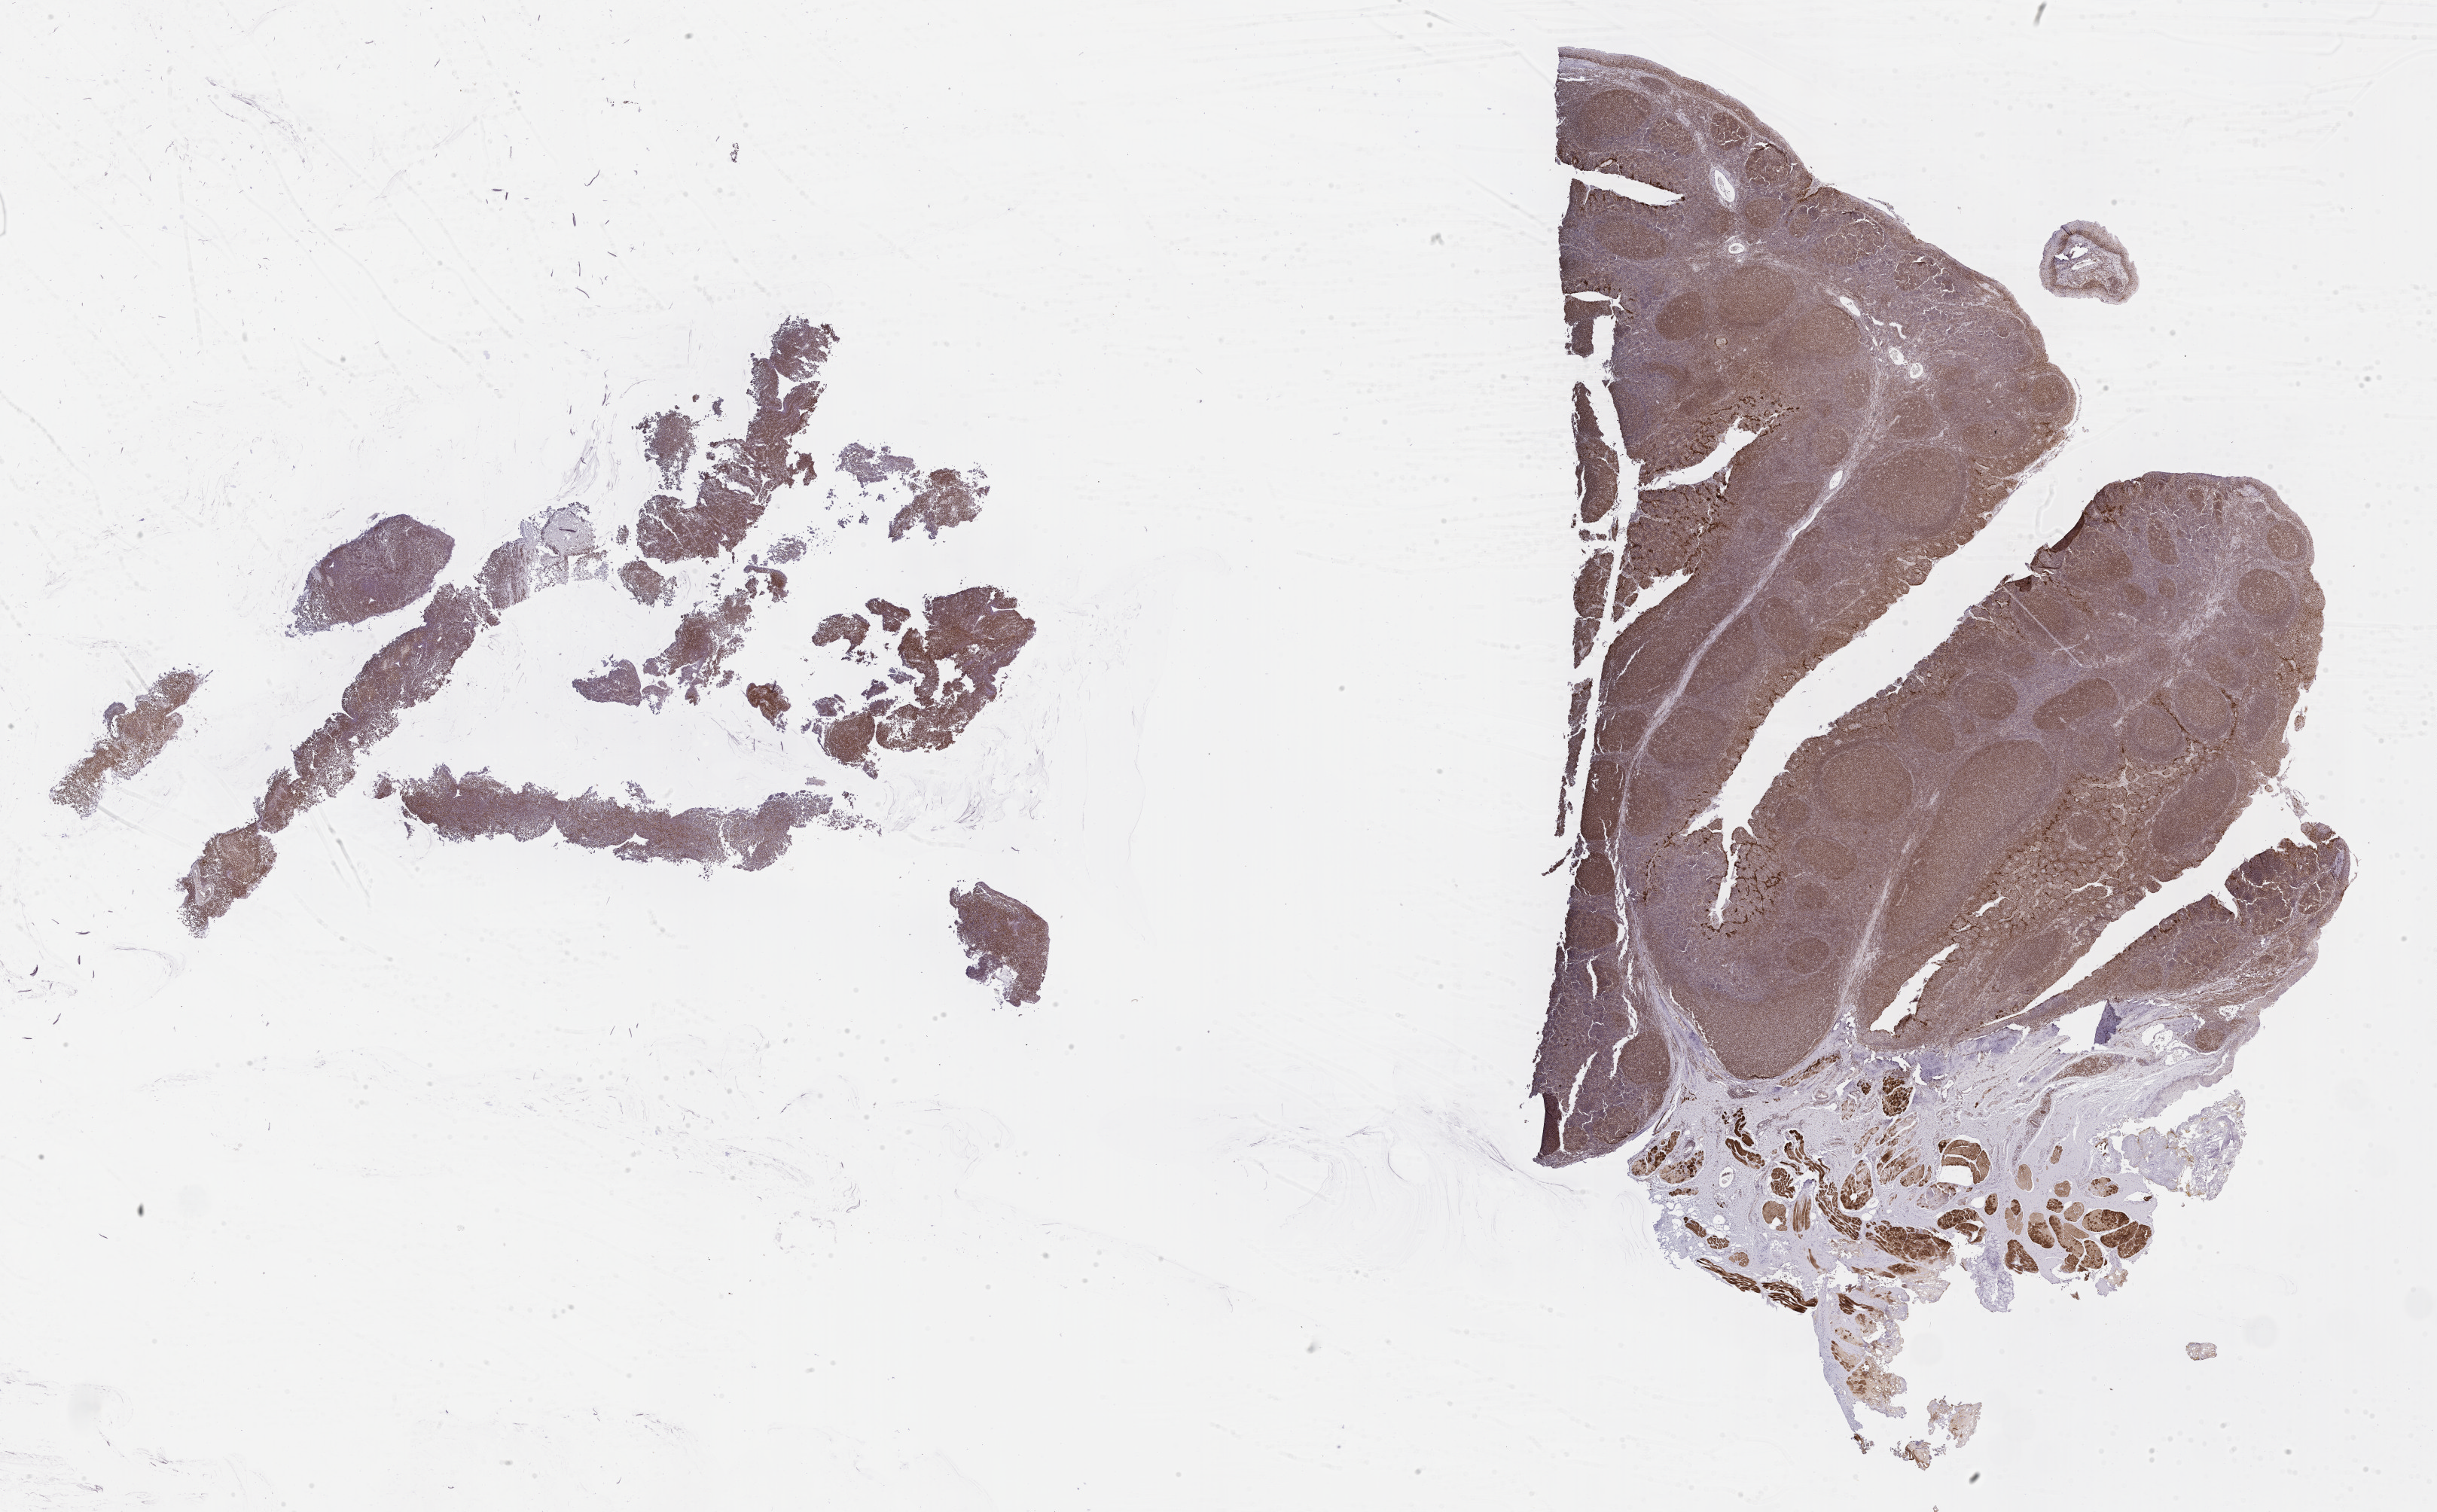
Immunohistochemistry (IHC) whole-slide image stained for BCL6, a low-resolution overview of the entire scanned area, about 26.2 x 16.2 mm. Tumor tissue. Anatomic site: kidney. Patient: male, age at initial diagnosis 3 years.
Histologic diagnosis: Burkitt lymphoma, NOS.